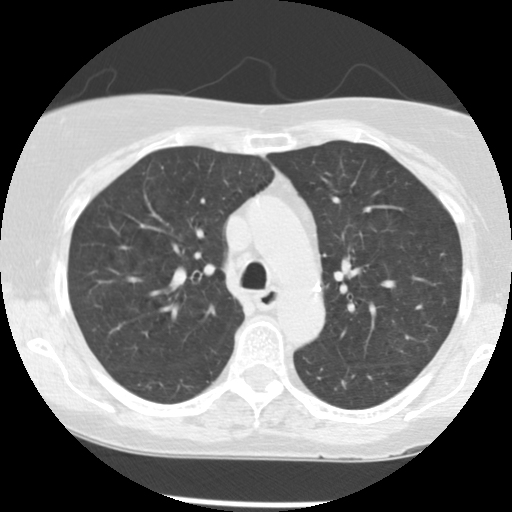
Low-dose screening chest CT, axial slice; second annual screen; lung window (W 1500 / L -600 HU); 120 kVp; 512 × 512 image matrix, field of view 292 × 292 mm. Female, age 63 years at enrolment.
- Lesion marked by an expert reader, bounding box <325,367,365,402> (left, top, right, bottom; pixels).
- Reader record for this screening exam (exam-level; its link to the box is not recorded): non-calcified nodule or mass ≥4 mm, left lower lobe, 7 × 6 mm, poorly defined margins, soft tissue attenuation, pre-existing on the prior screen: yes; interval growth: yes.
- Official screen result: positive, other.
- Participant outcome: lung cancer diagnosed 460 days after this screen — squamous cell carcinoma, NOS, left lower lobe, moderately differentiated (G2), stage IB (AJCC 6th edition), 15 mm at pathology.